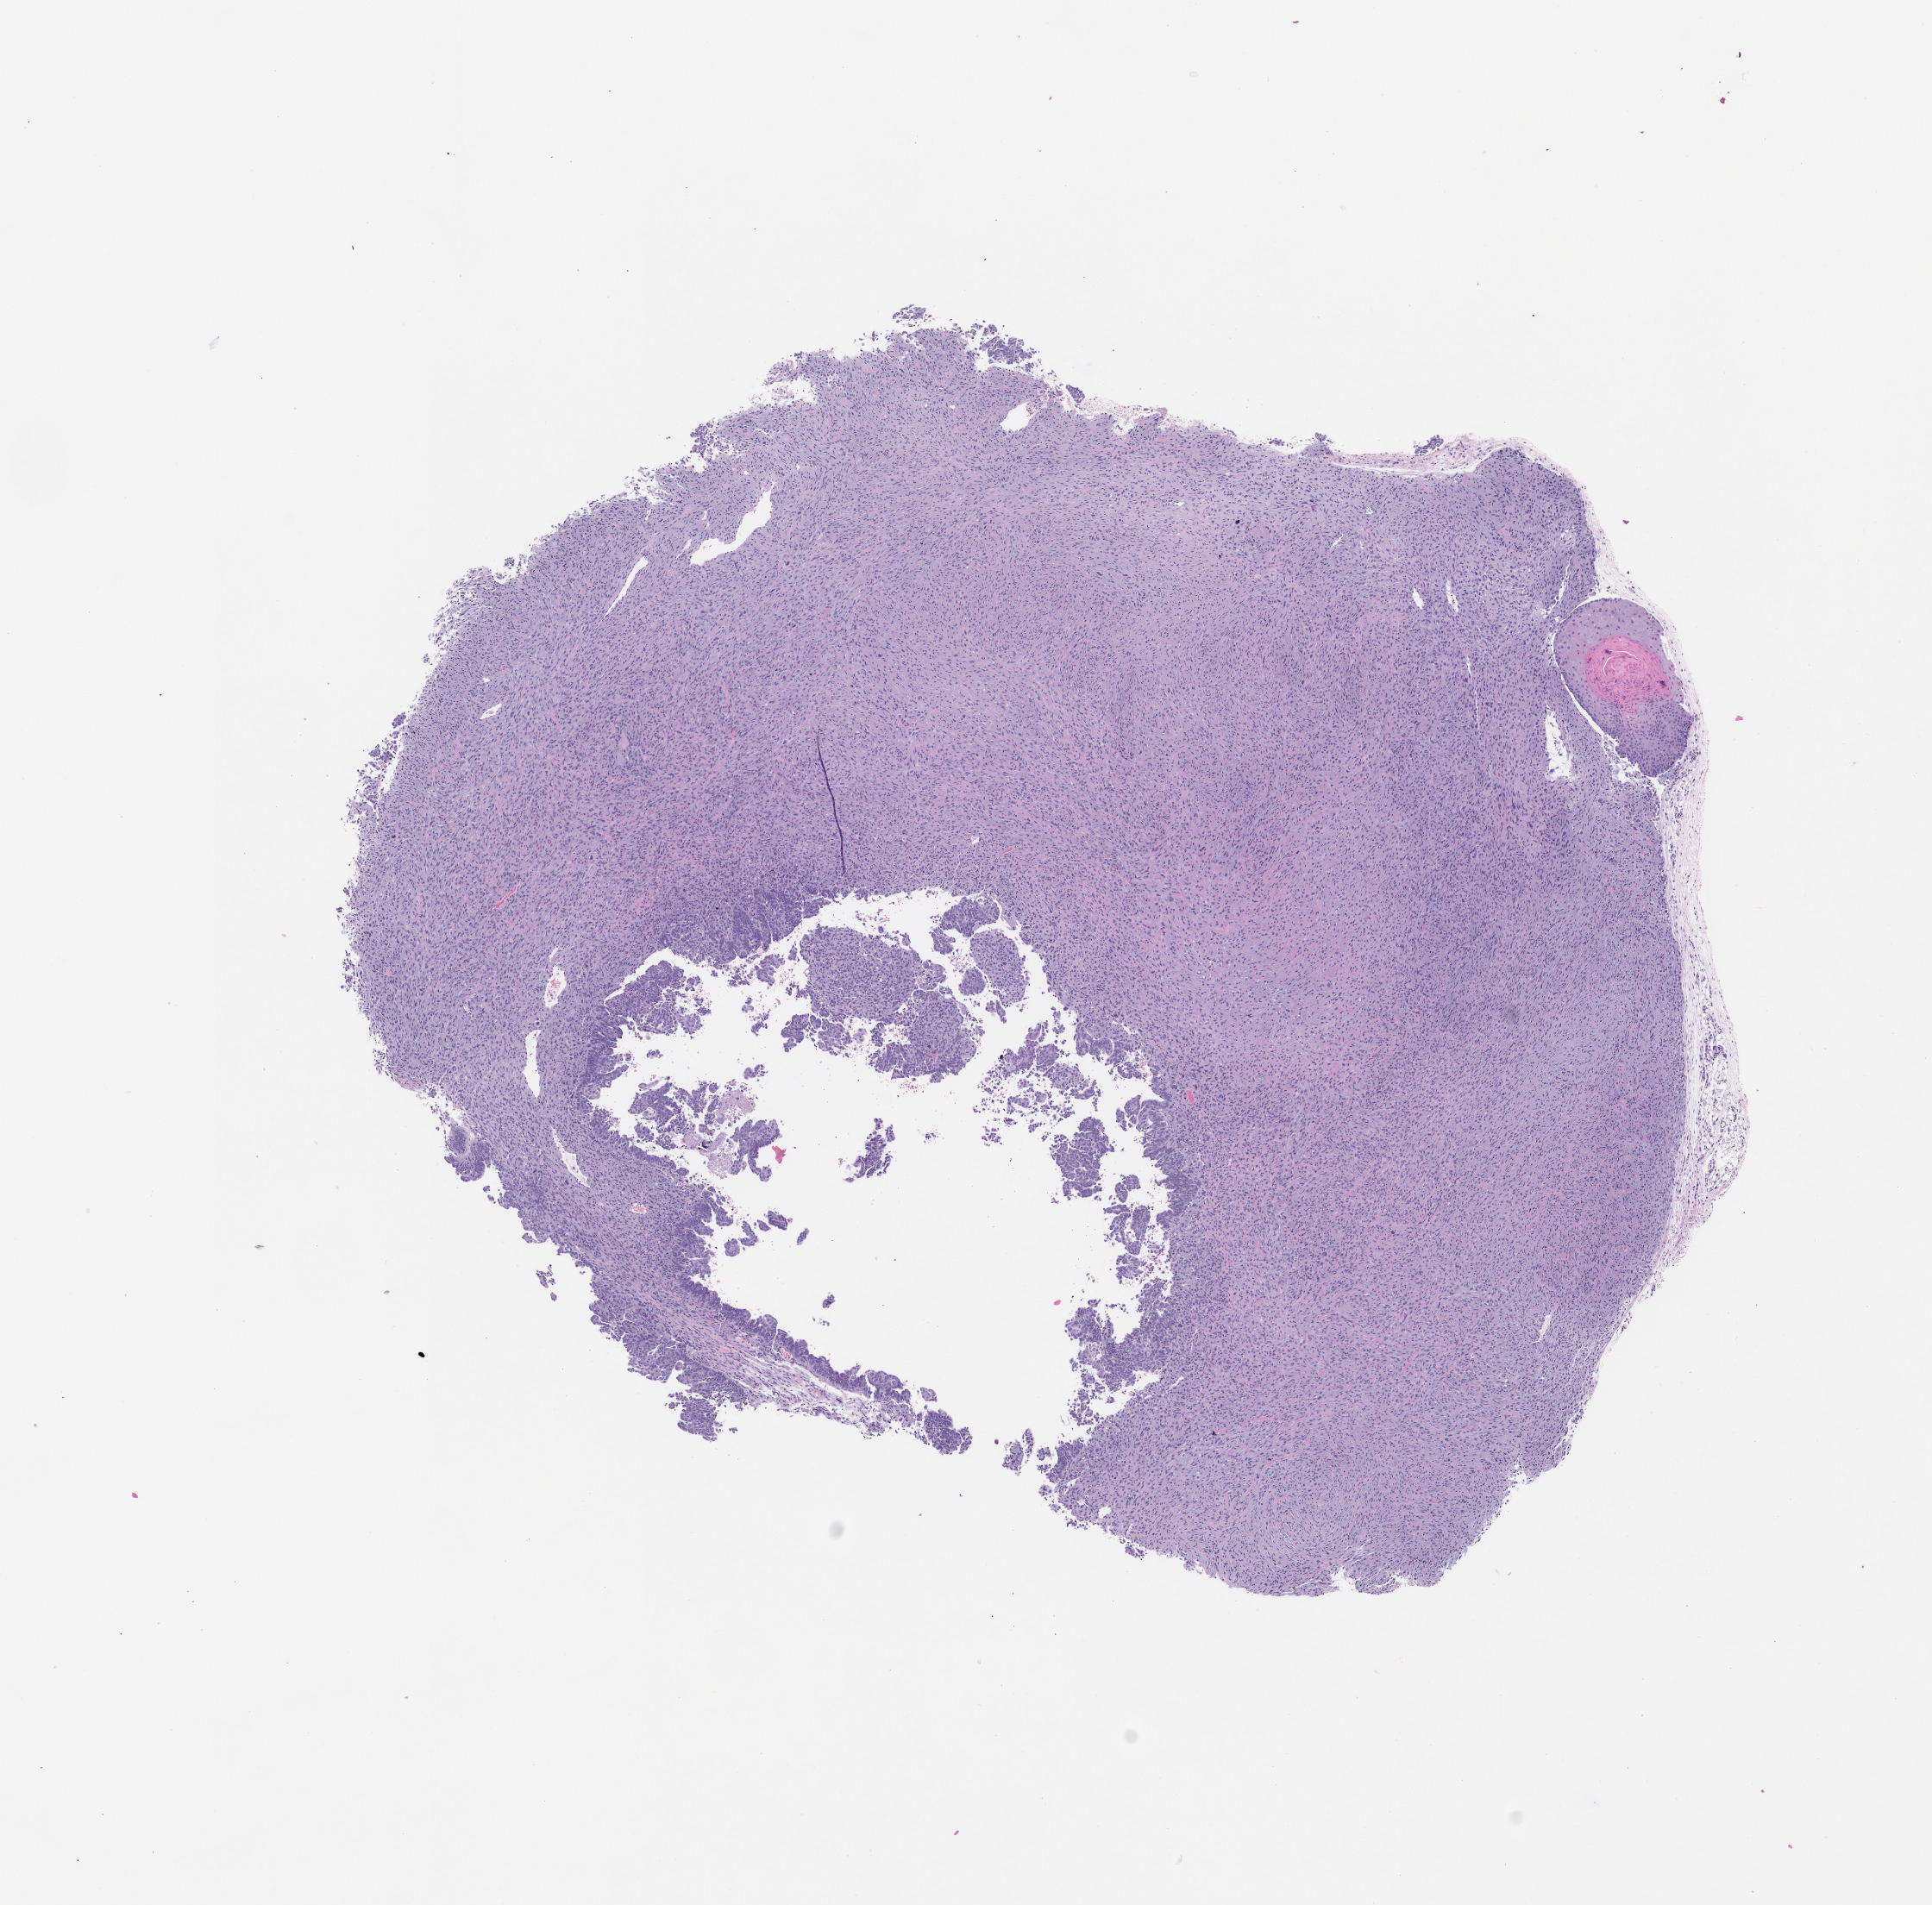
Whole-slide image, H&E: patient-derived xenograft (human tumor grown in a mouse), passage 0, low-resolution overview of the scanned area, about 9.0 x 8.9 mm; FFPE section; tumor site category: female genital tract.
Originating patient diagnosis: Carcinosarcoma.